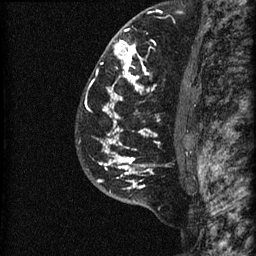
Breast MRI (dynamic contrast-enhanced), one sagittal slice. Slice 46 of 60 in the series (ordered by position). Dynamic contrast-enhanced series, image 2 of 3 at this slice position (ordered by acquisition). 1.5 T. TE 4.2 ms, TR 22.7 ms. 1.5 mm slice thickness. 256 × 256 image matrix, field of view 180 × 180 mm. Female patient, age 48 years. Case-level facts recorded for this patient, not image findings: setting: breast cancer imaged before/during neoadjuvant chemotherapy; receptor status: triple-negative.
Annotated regions visible in this slice (semi-automatic segmentation, software-assisted and operator-edited):
- analysis volume of interest (the breast-tissue region the enhancement analysis was run in; not a lesion): bounding box <81,23,186,202> (left, top, right, bottom; pixels)
- tumour enhancement mask (voxels above the 90 % enhancement threshold inside the analysis volume of interest): <89,40,159,189>